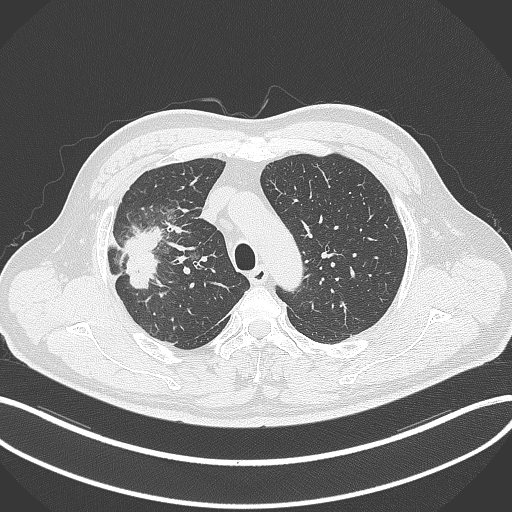
Chest CT, one axial slice; slice 257 of 348 in the series (ordered by position); reconstruction kernel B70f; 120 kVp; lung window (W 1500 / L -600 HU); 1 mm slice thickness; 512 × 512 image matrix. Male patient, age 55 years. From the clinical record (not read from this slice): clinical TNM (as recorded): T3 N2 M1.
Annotated regions visible in this slice (rectangle marked by the reading radiologist):
- lung tumour (recorded histology: adenocarcinoma): bounding box (x1, y1, x2, y2) in pixels: (121, 224, 163, 293)